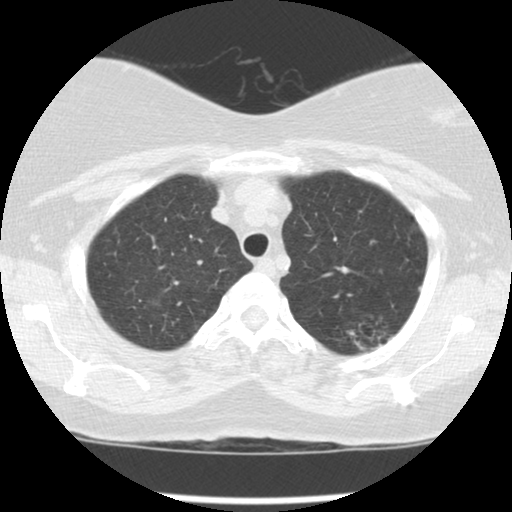
Axial slice from a low-dose chest CT screening exam, third screening round (two years after baseline), lung window (W 1500 / L -600 HU), slice 20 of 127 in the series. Female, age 56 years at enrolment. Current smoker at enrolment.
Expert-annotated lung lesion, box from (x=332, y=301) to (x=406, y=357) px. The screening reader recorded 4 non-calcified nodules or masses ≥4 mm on this exam (left upper lobe, left upper lobe, left upper lobe, right upper lobe); which of them this box marks is not recorded.